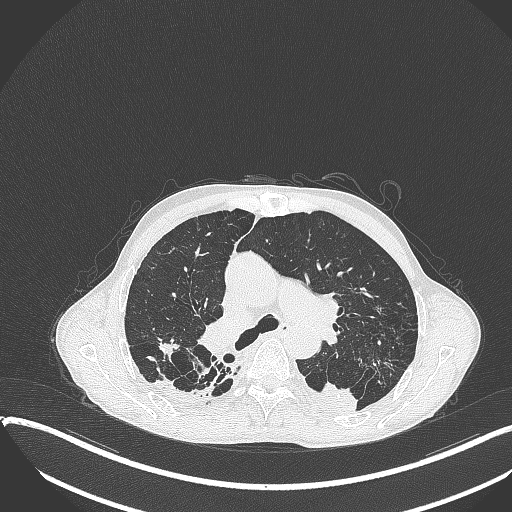
Chest CT, one axial slice. Slice 254 of 401 in the series (ordered by position). Reconstruction kernel B70f. 120 kVp. Lung window (W 1500 / L -600 HU). 1 mm slice thickness. 512 × 512 image matrix, field of view 400 × 400 mm. Male patient, age 57 years. Case-level facts recorded for this patient, not image findings: clinical TNM (as recorded): T4 N0 M0.
Annotated regions visible in this slice (bounding box drawn by a radiologist):
- lung tumour (recorded histology: squamous cell carcinoma): bounding box <300,378,361,419> (left, top, right, bottom; pixels)